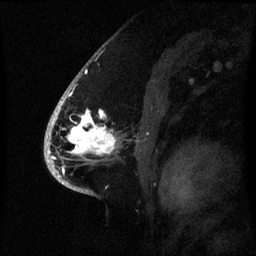
Breast MRI (dynamic contrast-enhanced), one sagittal slice; slice 44 of 60 in the series (ordered by position); dynamic contrast-enhanced series, image 2 of 3 at this slice position (ordered by acquisition); 1.5 T; TE 4.2 ms, TR 8.4 ms; 2.1 mm slice thickness; 256 × 256 image matrix, field of view 220 × 220 mm. Female patient, age 53 years. Case-level facts recorded for this patient, not image findings: setting: breast cancer imaged before/during neoadjuvant chemotherapy; receptor status: HR-positive, HER2-negative.
Outlined on this slice (semi-automatic segmentation, software-assisted and operator-edited):
- analysis volume of interest (the breast-tissue region the enhancement analysis was run in; not a lesion): bounding box <52,90,124,171> (left, top, right, bottom; pixels)
- tumour enhancement mask (voxels above the 70 % enhancement threshold inside the analysis volume of interest): <53,98,116,155>